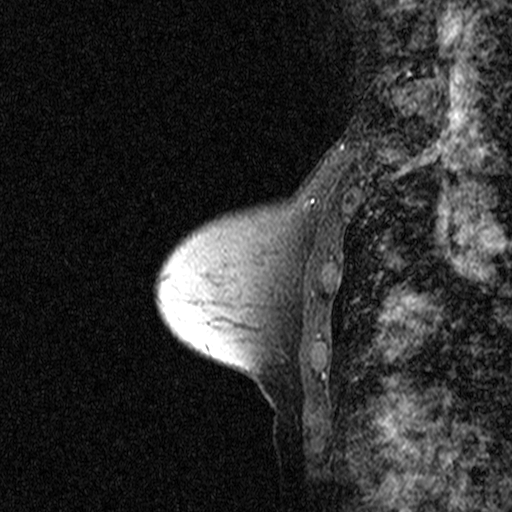
Breast MRI (dynamic contrast-enhanced), one sagittal slice; slice 15 of 44 in the series (ordered by position); dynamic contrast-enhanced study with each time point stored as its own series, time point 2 of 3 at this slice position (early post-contrast, ordered by acquisition time); 1.5 T; TE 4.5 ms, TR 11 ms; 2.27 mm slice thickness; 512 × 512 image matrix, field of view 200 × 200 mm. Patient: female, 53 years. Case-level facts recorded for this patient, not image findings: setting: breast cancer imaged before/during neoadjuvant chemotherapy; receptor status: HR-positive, HER2-negative.
Annotated regions visible in this slice (semi-automatic segmentation, software-assisted and operator-edited):
- analysis volume of interest (the breast-tissue region the enhancement analysis was run in; not a lesion): bounding box [x1, y1, x2, y2] px = [200, 178, 317, 309]
- tumour enhancement mask (voxels above the 90 % enhancement threshold inside the analysis volume of interest): [308, 199, 314, 208]